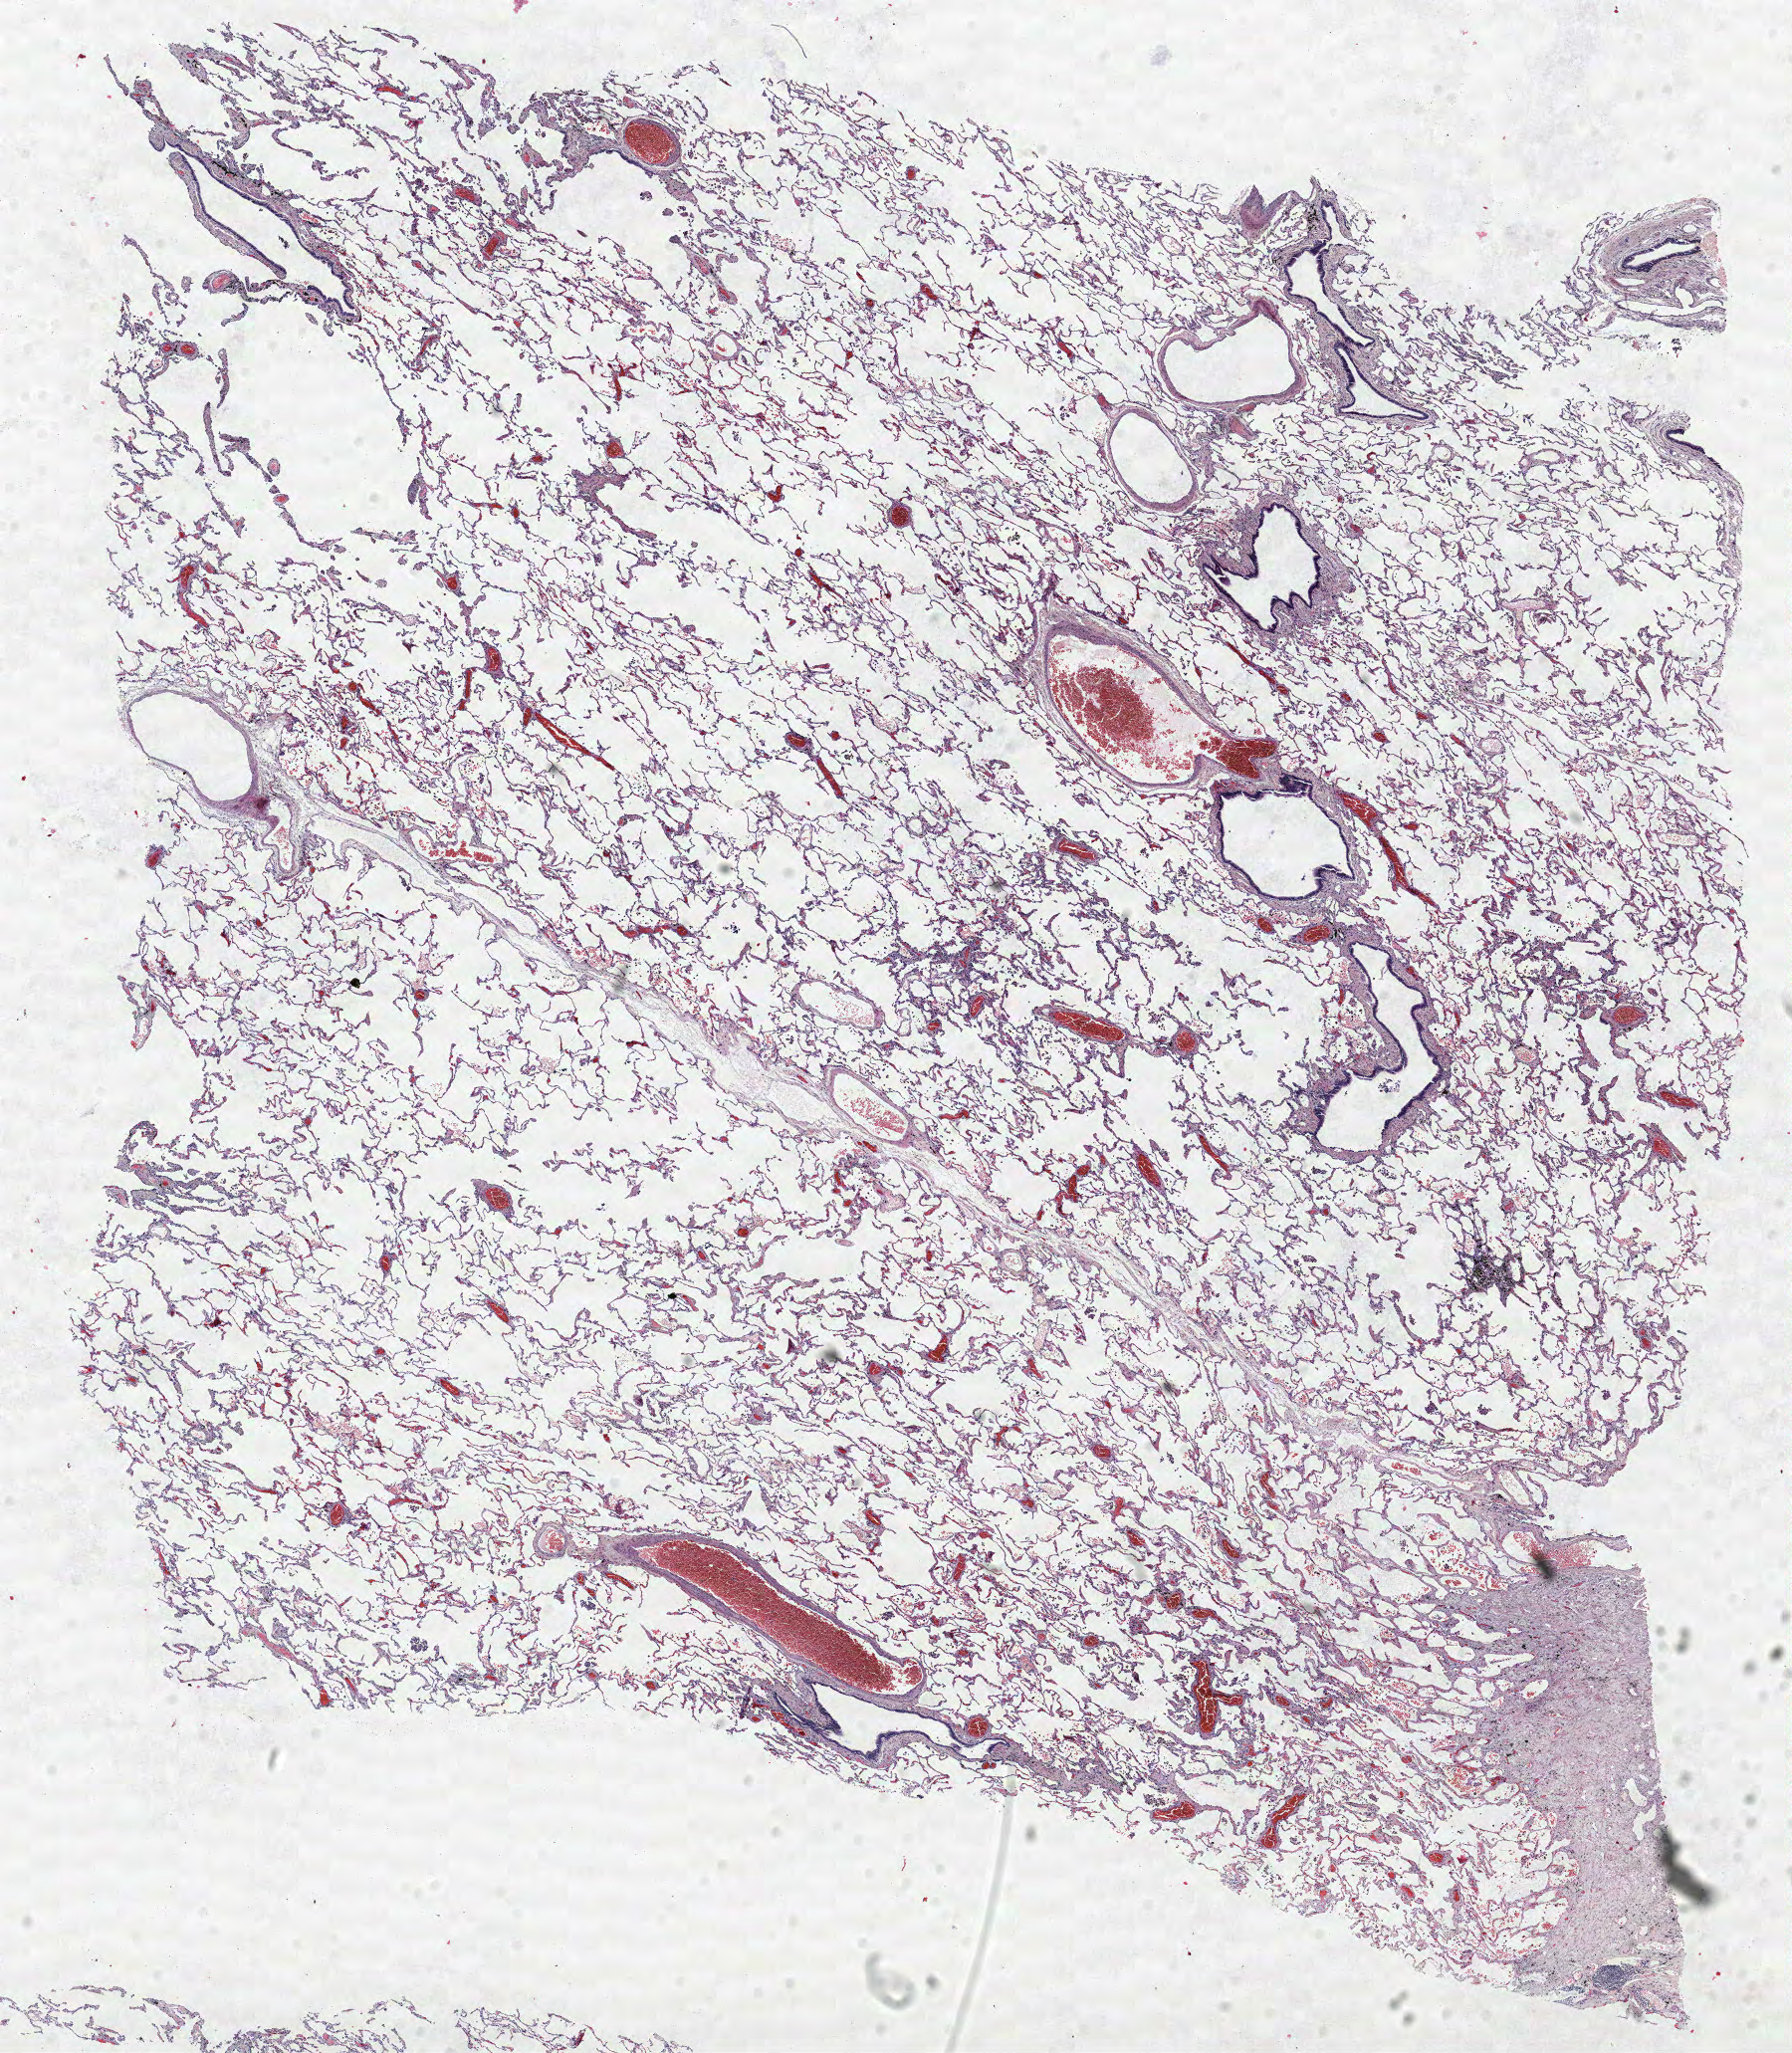
Whole-slide histology image, H&E-stained — low-resolution overview of the scanned area, about 14.4 x 16.5 mm. FFPE section. Lung. Male, age 68 at enrolment. Current smoker at enrolment. Grade: undifferentiated (G4).
* stage (AJCC 6th edition): IIIB
* primary tumour location (clinical record): right upper lobe
* participant's lung-cancer diagnosis: Combined small cell carcinoma (ICD-O-3 8045/3)
* ICD-O-3 topography: upper lobe of lung (C34.1)
* tumour size (pathology): 30 mm